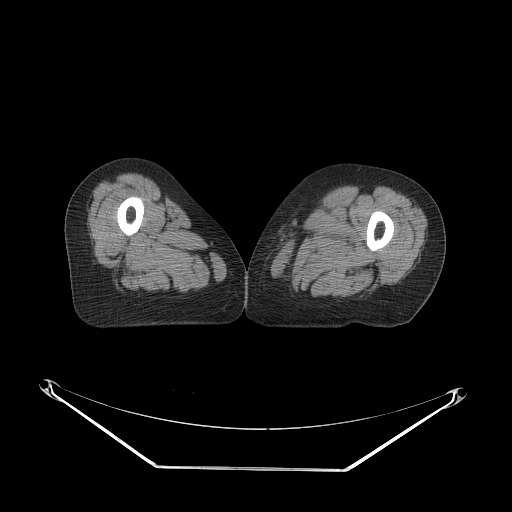
CT of an extremity soft-tissue mass (from a PET/CT study), one axial slice; position 53 of 91 along the scan axis; reconstruction kernel STANDARD; soft-tissue window (W 400 / L 40 HU); 512 × 512 image matrix, field of view 500 × 500 mm. Female patient. Case-level facts recorded for this patient, not image findings: histological type: pleomorphic leiomyosarcoma; grade: high; site of the primary tumour: left thigh.
Structures marked on this image (expert contour drawn on MRI and transferred to this co-registered scan by the dataset authors):
- gross tumour volume including surrounding oedema: bounding box <274,201,321,225> (left, top, right, bottom; pixels)